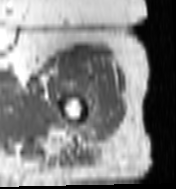
MRI of an extremity soft-tissue mass, one axial slice; position 92 of 100 along the scan axis; MR volume resampled by the dataset authors to the PET/CT grid (not the native acquisition matrix); 3.27 mm slice thickness; 176 × 189 image matrix. Female patient. Case-level facts recorded for this patient, not image findings: histological type: undifferentiated – high grade; grade: high; site of the primary tumour: left thigh.
Structures marked on this image (expert contour drawn on MRI and transferred to this co-registered scan by the dataset authors):
- gross tumour volume including surrounding oedema: bounding box <89,100,109,135> (left, top, right, bottom; pixels)